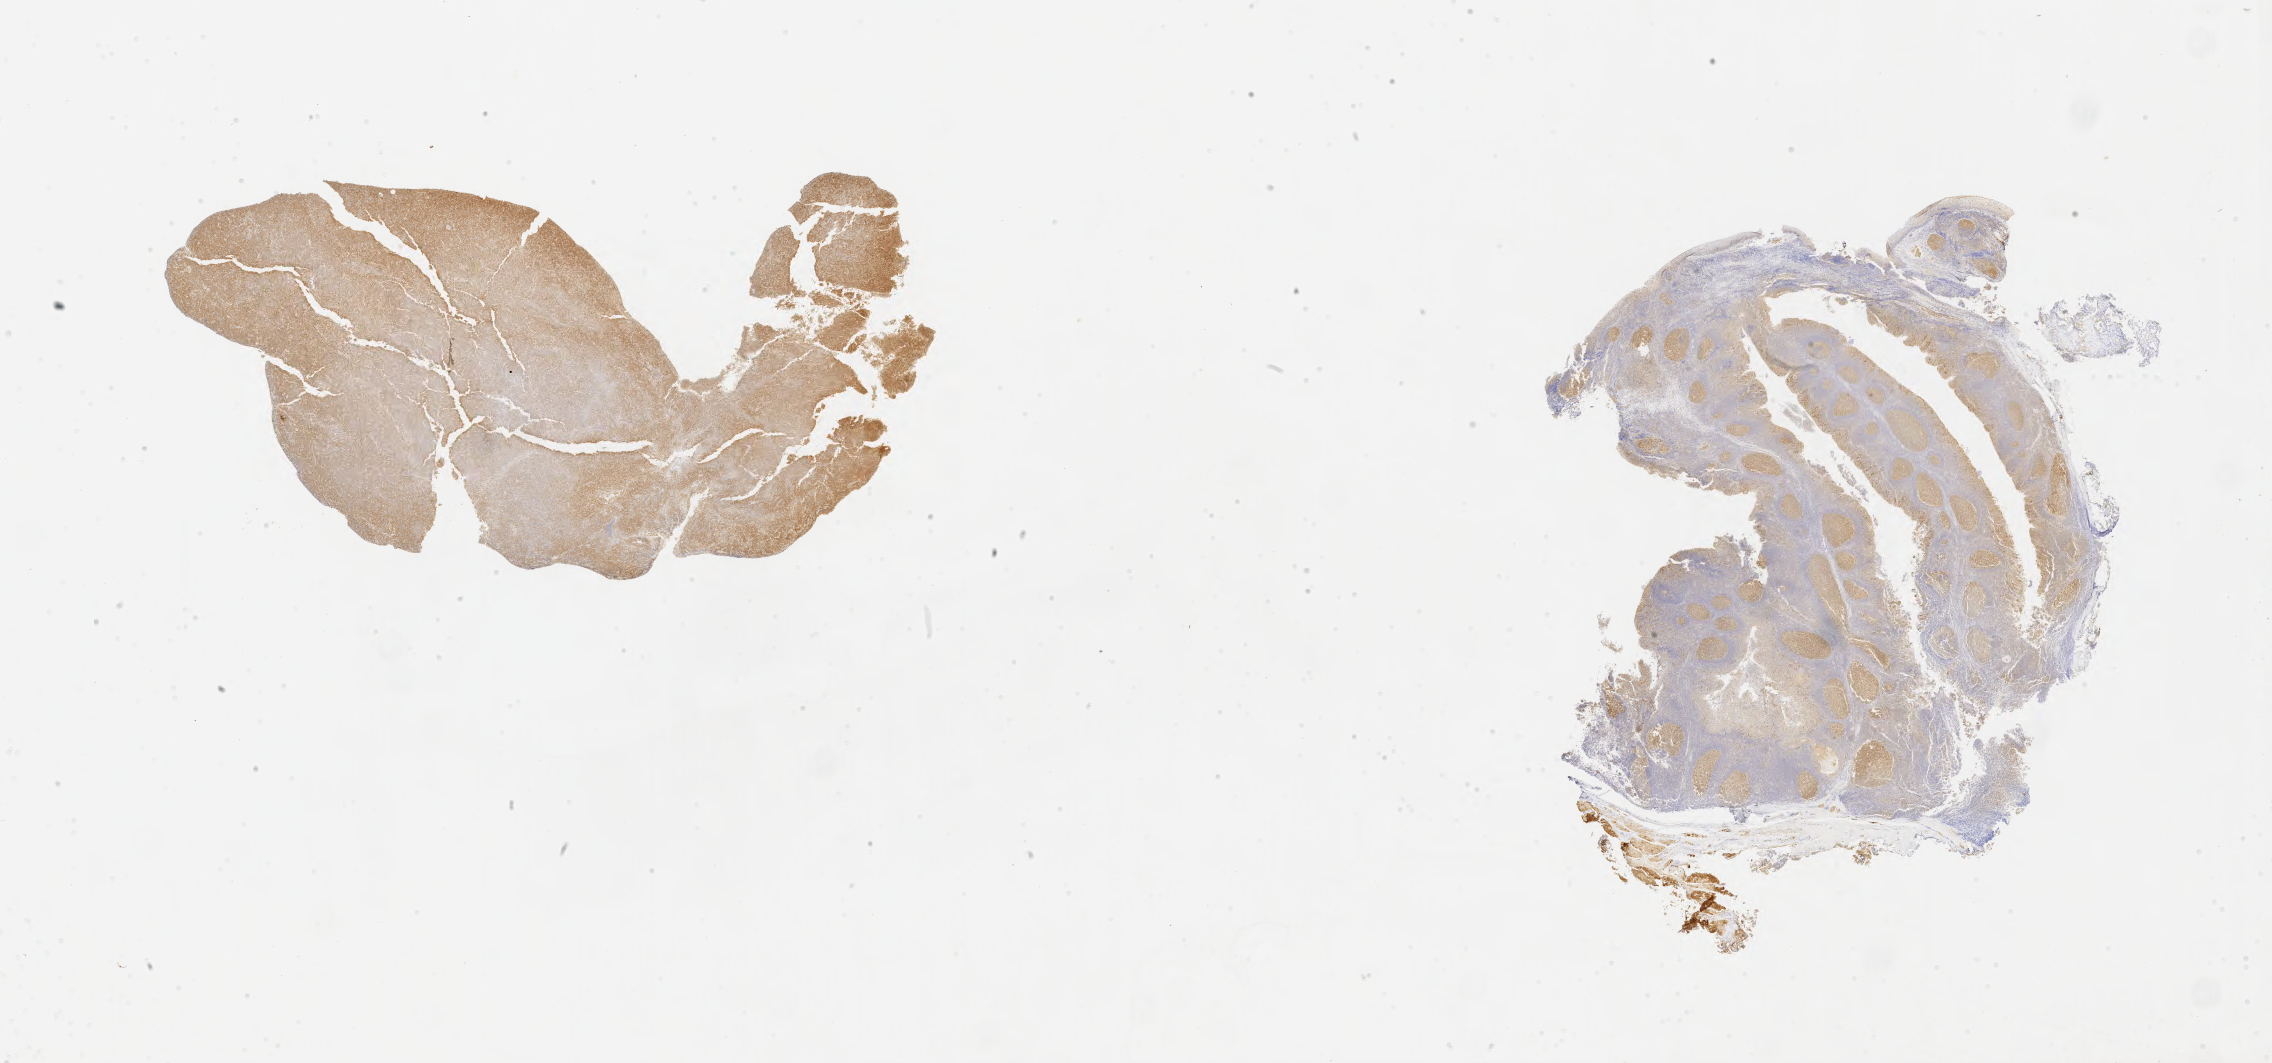
Whole-slide image, immunohistochemical stain for BCL6 — shown as a low-resolution overview of the whole scanned area (about 36.7 x 17.2 mm); specimen: tumor tissue; site: lymph node of head and neck. Male patient; age at initial diagnosis 5 years.
Diagnosis: Burkitt lymphoma, NOS.